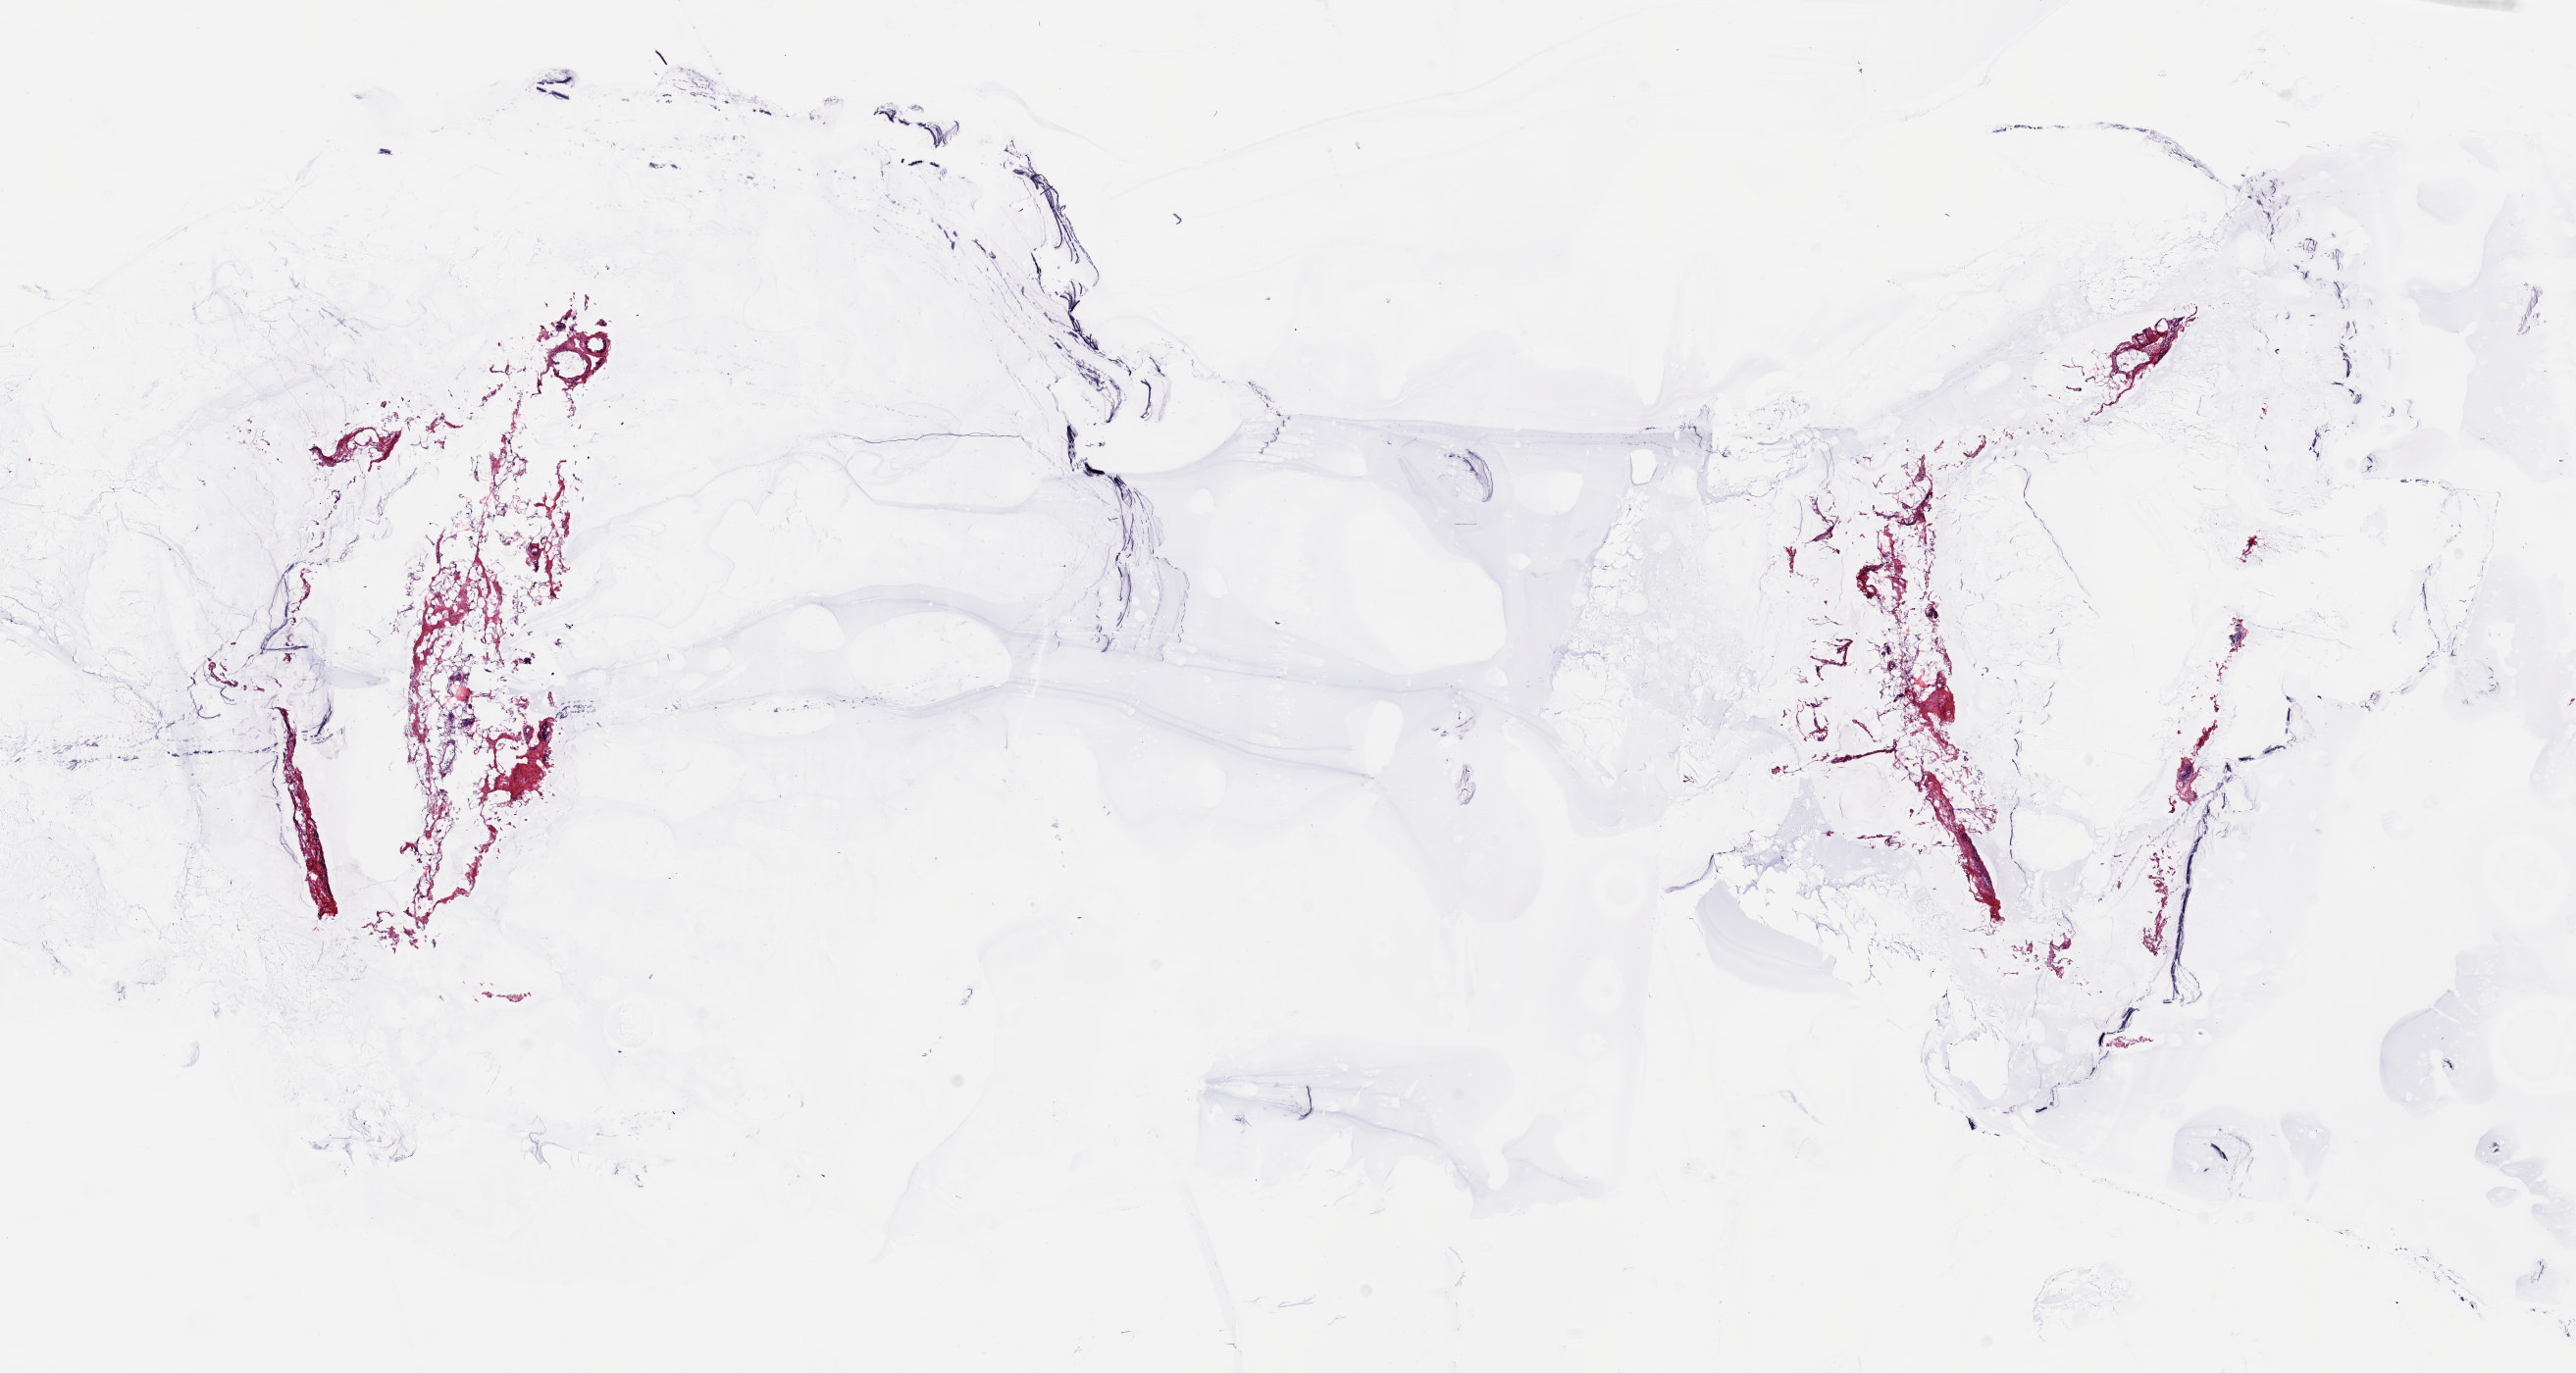
Digitized Hematoxylin and eosin (H&E) stained tissue section (whole slide) — low-resolution overview of the scanned area, about 20.8 x 11.1 mm, frozen section from the top of the tissue portion, breast, solid tissue normal (non-tumour tissue) sample. Patient: female, age at initial diagnosis 62 years. Slide review estimates, as recorded: tumour cells 0%, tumour nuclei 0%, normal cells 100%, stromal cells 0%, necrosis 0%. Infiltration values recorded for this section: lymphocyte infiltration 1%, monocyte infiltration 0%, neutrophil infiltration 0%.
This section: solid tissue normal sample (biorepository sample class). Patient diagnosis: Lobular carcinoma, NOS.